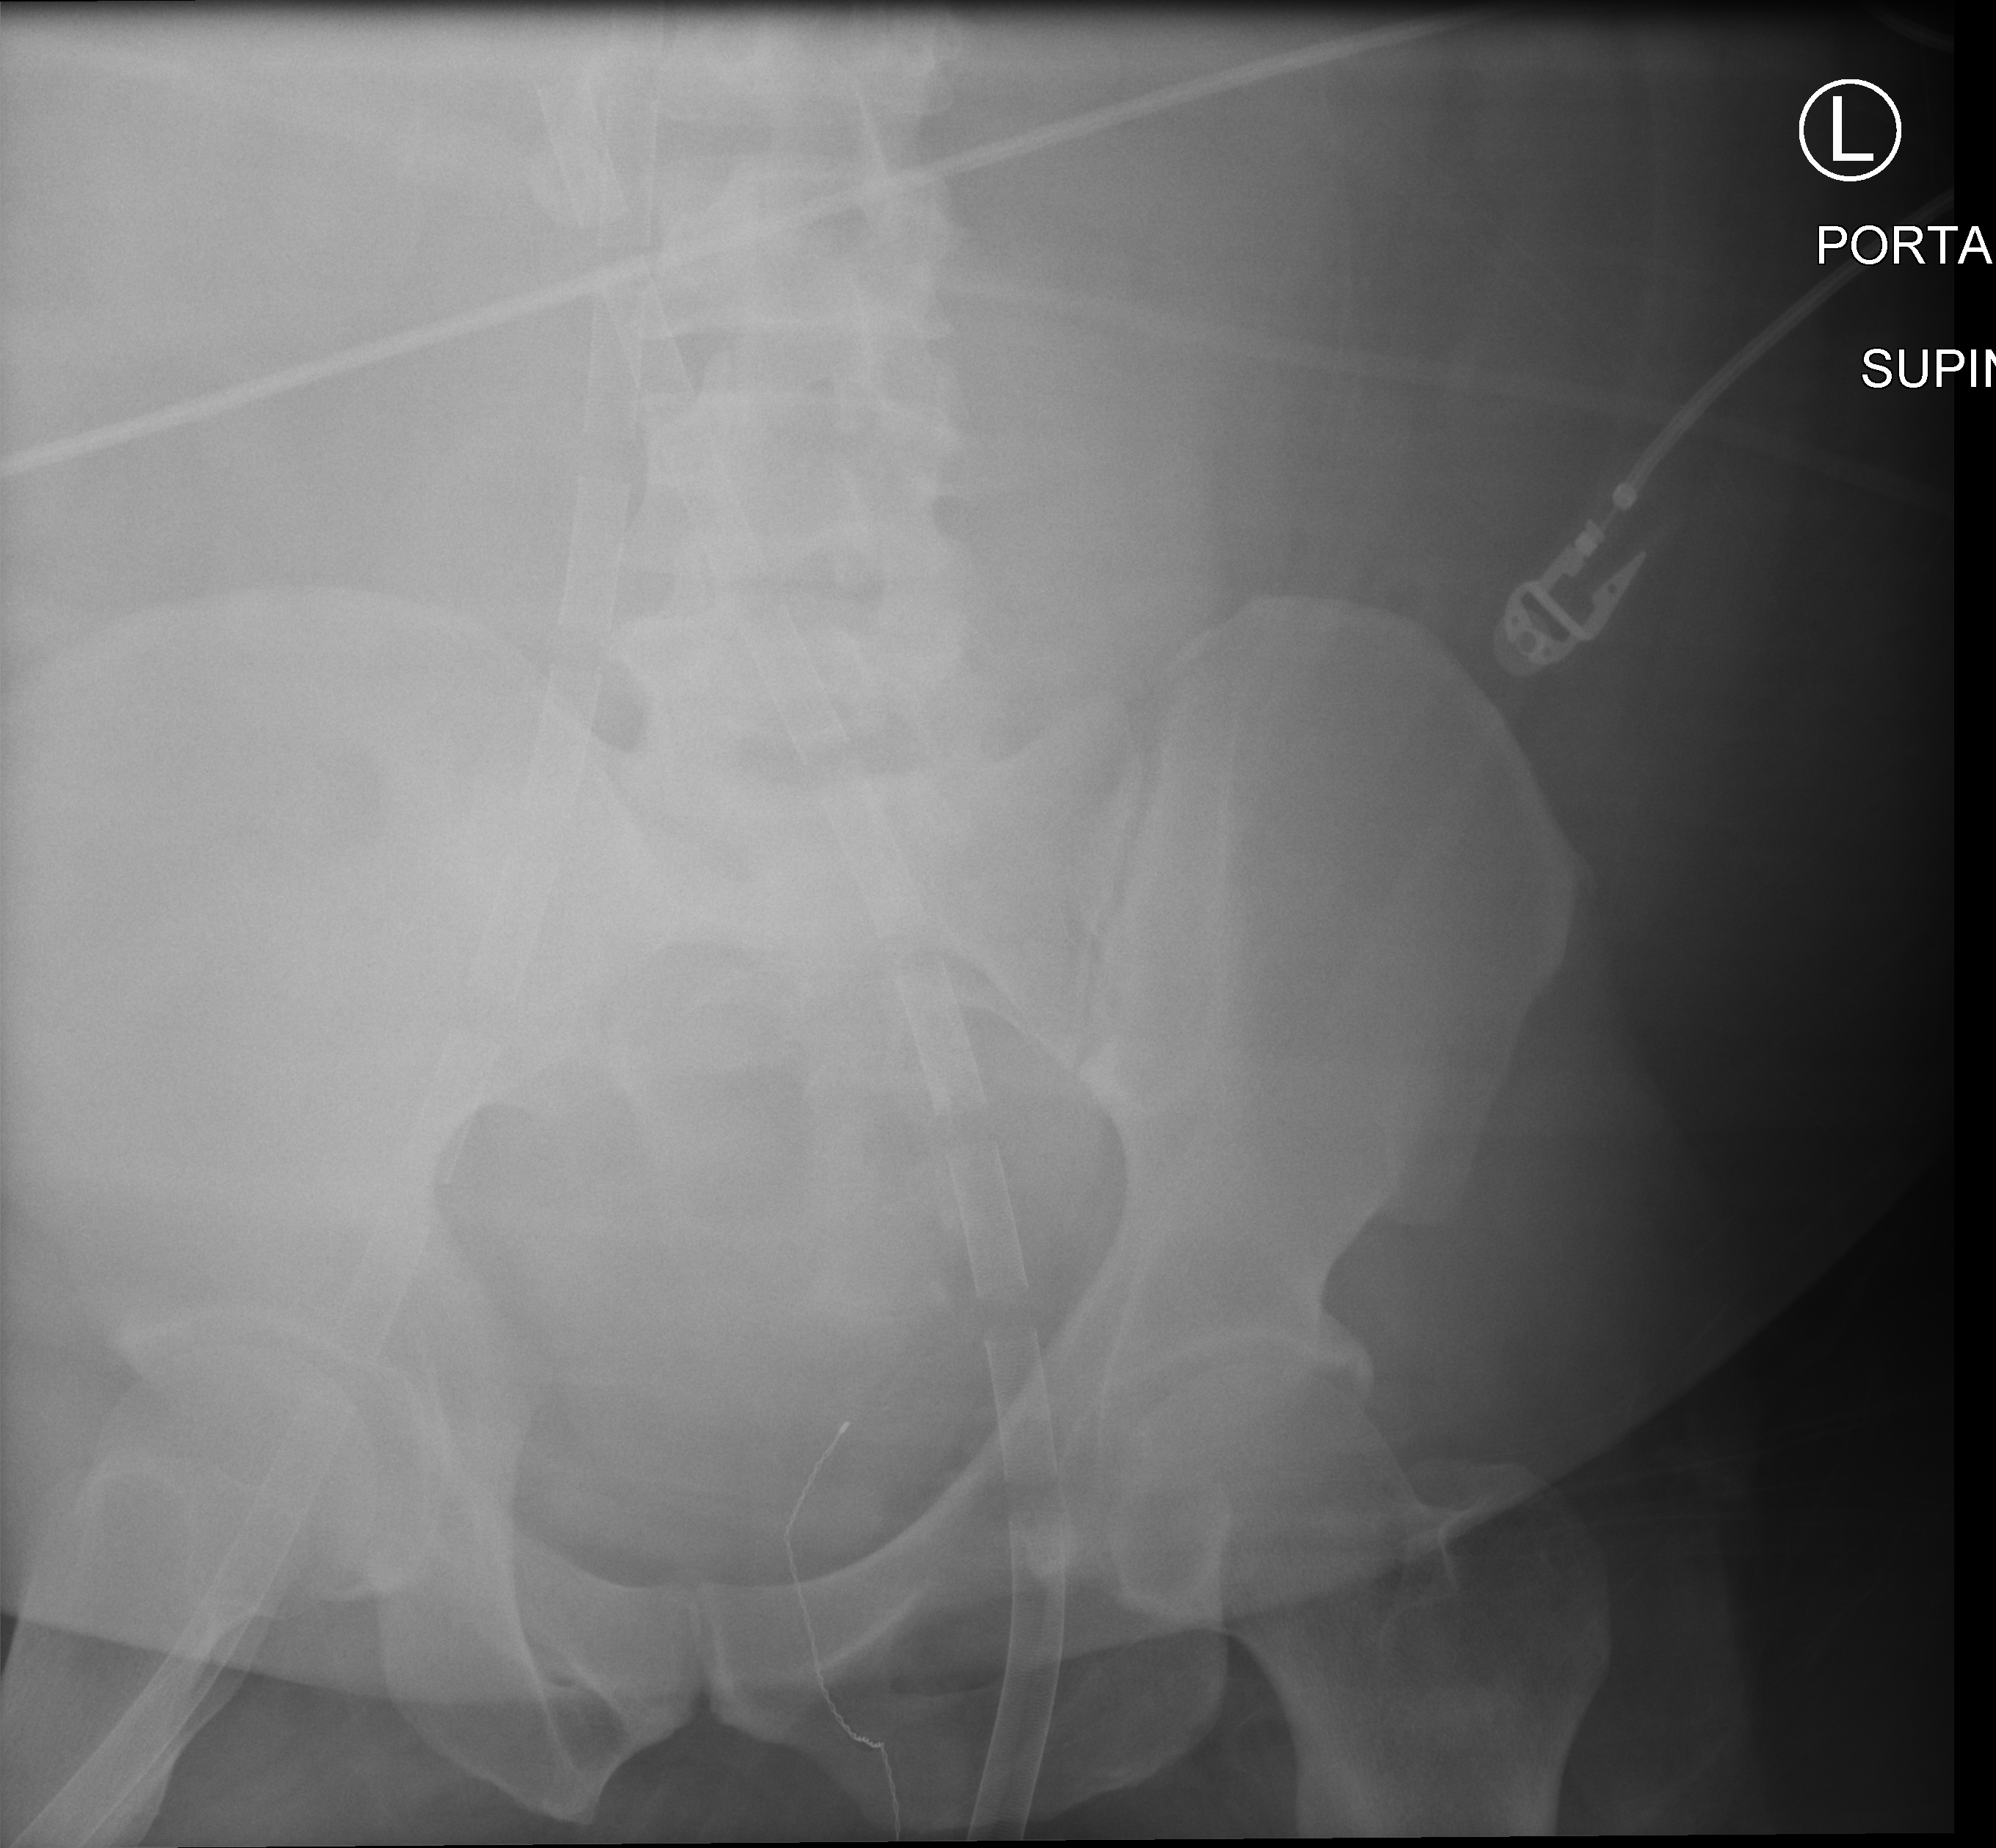
Bedside abdomen radiograph (computed radiography); anteroposterior (AP) projection. Patient hospitalised with COVID-19, aged 18–59 years.
Admission-level facts for this patient (not findings on this image; timing relative to this image not recorded): length of hospital stay: 15 days; COPD (admission record): no; mechanically ventilated during this hospital stay: yes.